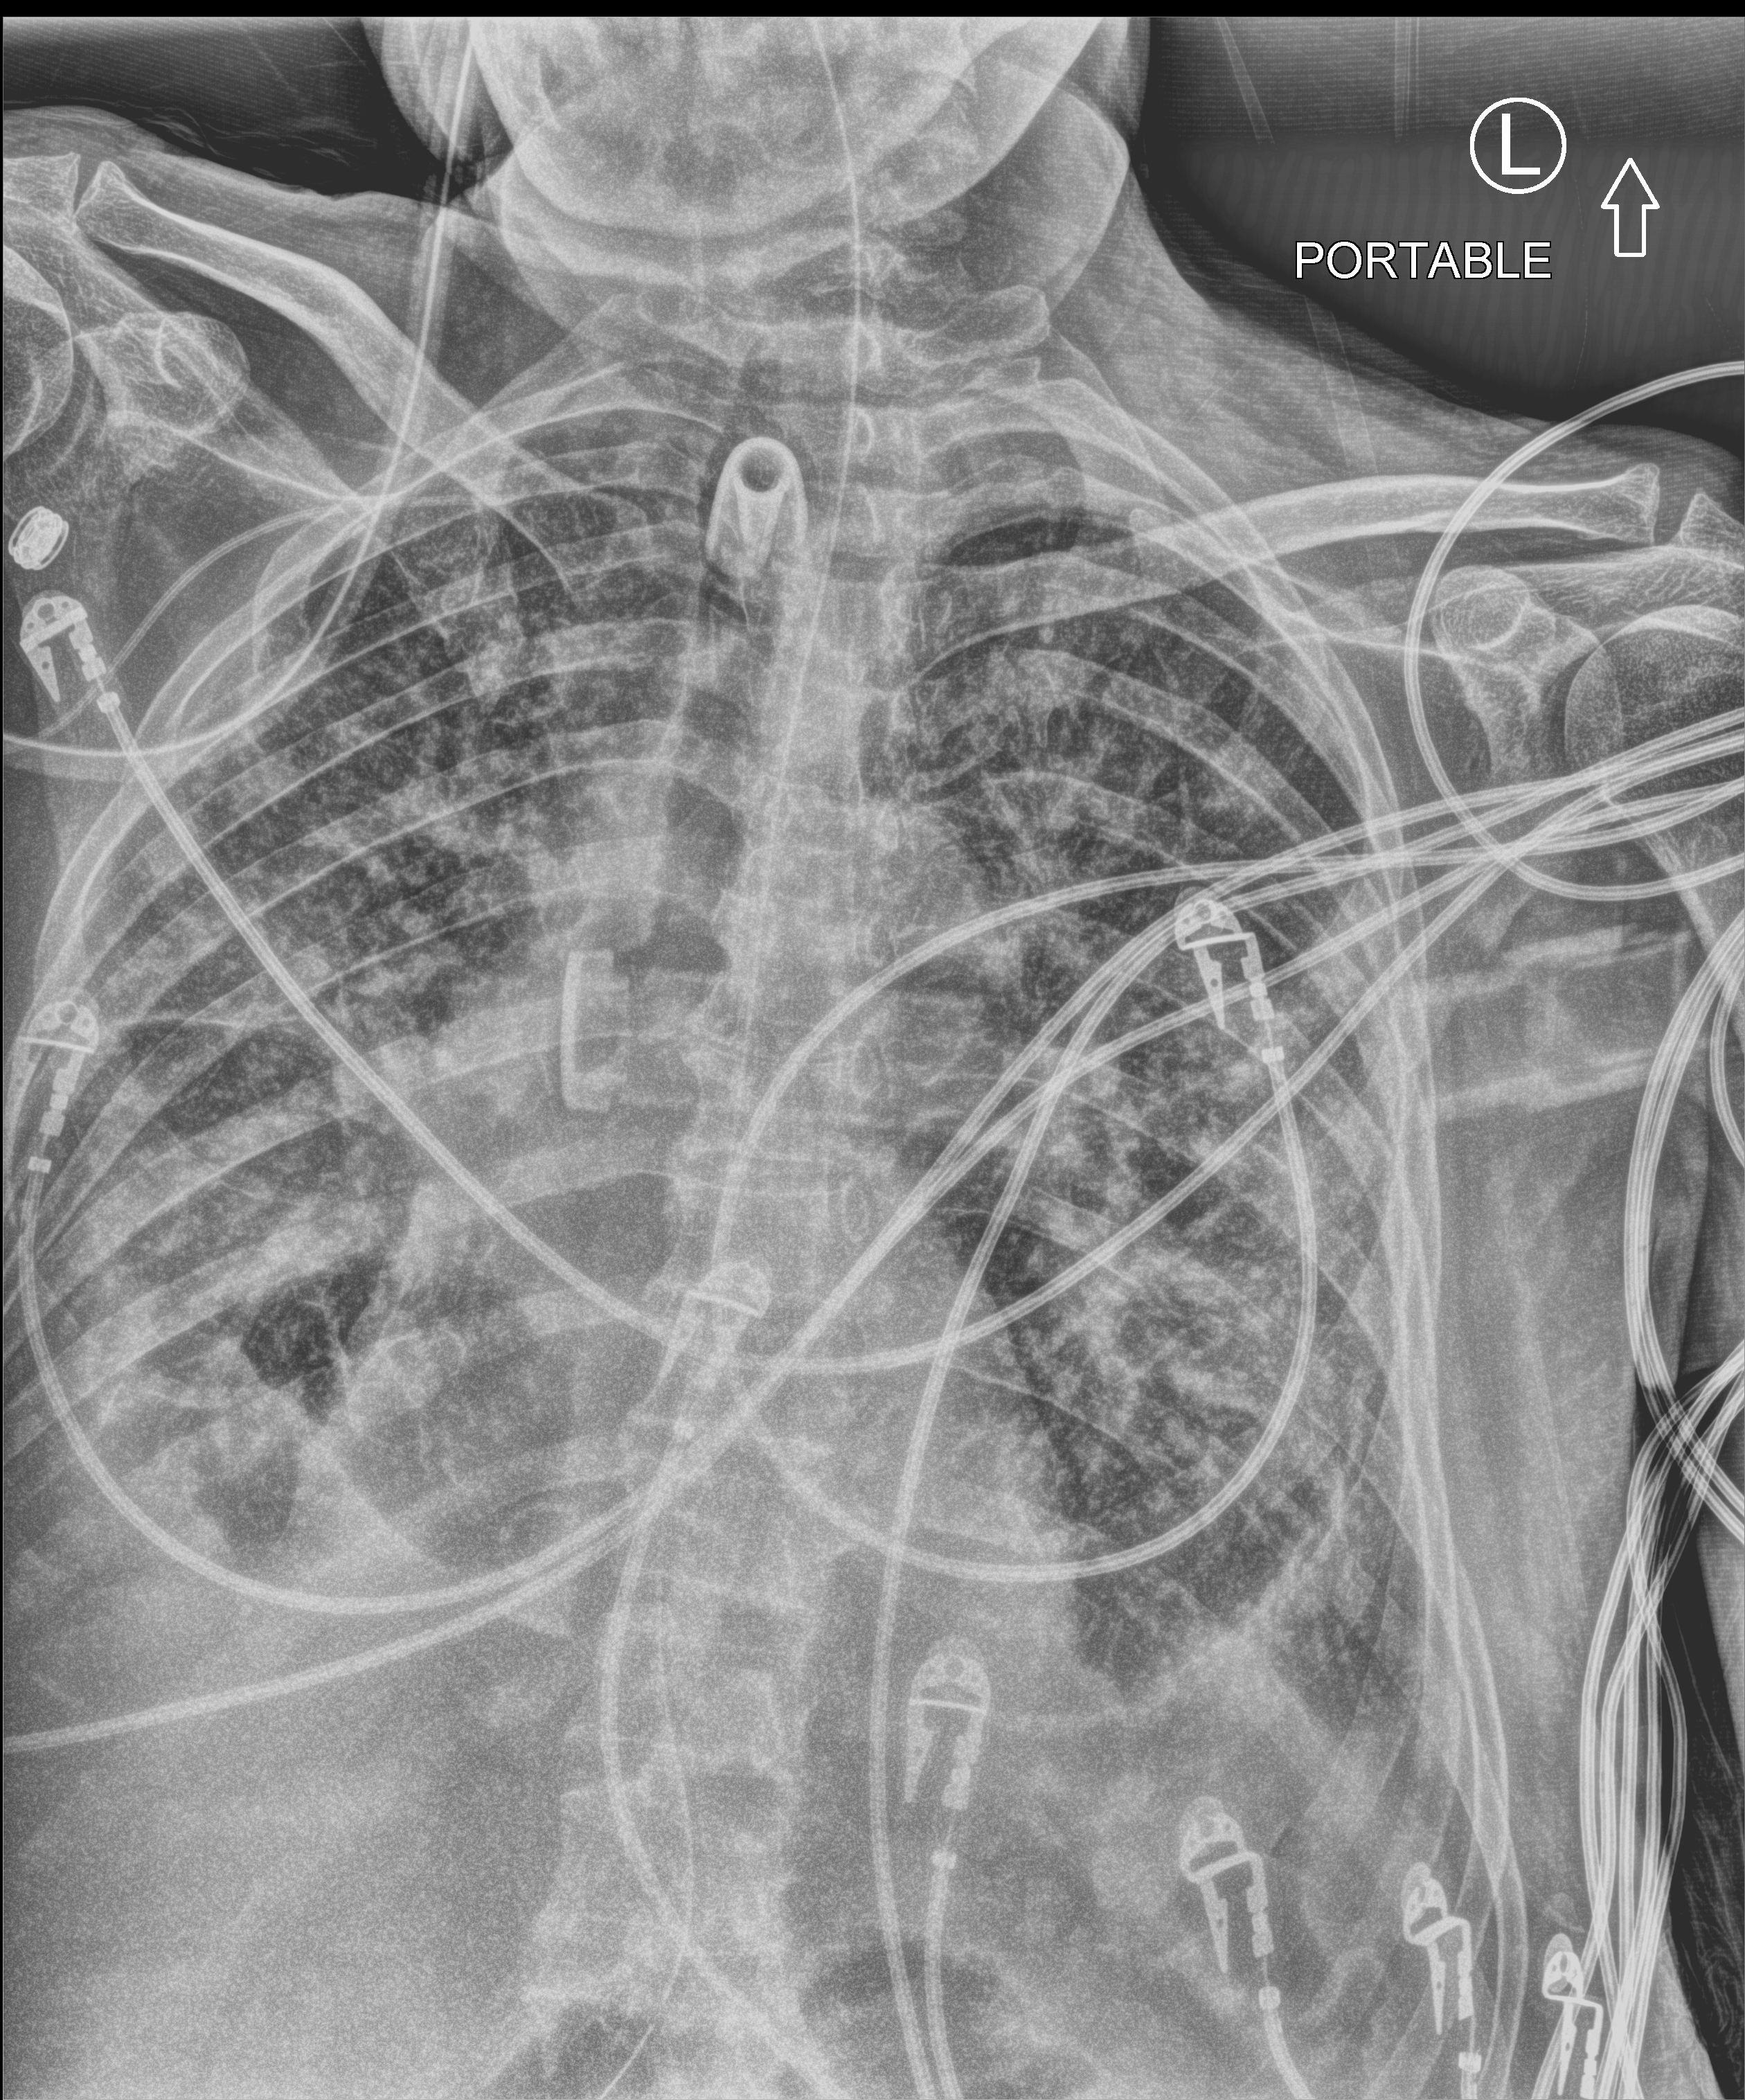
Chest X-ray (portable), anteroposterior (AP) projection. Patient hospitalised with COVID-19; male, aged 75–90 years.
Admission-level facts for this patient (not findings on this image; timing relative to this image not recorded):
- length of hospital stay: 70 days